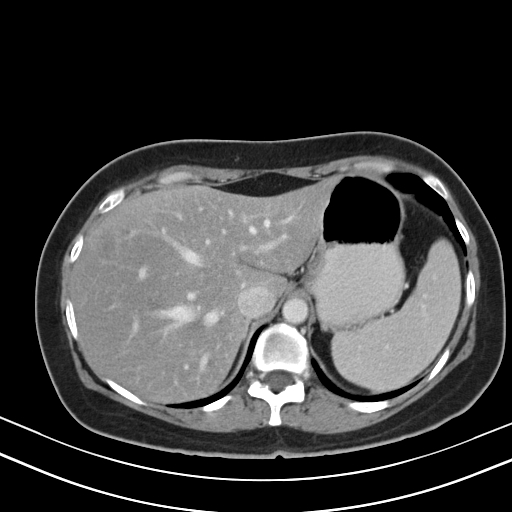
Contrast-enhanced abdominal CT, one axial slice; position 36 of 47 along the scan axis; 130 kVp; intravenous contrast given; soft-tissue window (W 400 / L 40 HU); 512 × 512 image matrix. Female patient. Case-level facts recorded for this patient, not image findings: diagnosis: colorectal cancer liver metastases, imaged before liver resection; multiple liver metastases: no; largest metastasis: 3.5 cm; disease in both lobes: no.
Annotated regions visible in this slice (expert manual segmentation):
- hepatic veins: box from (x=154, y=212) to (x=292, y=365) px
- liver: (x=74, y=184)–(x=329, y=400)
- planned liver remnant (the part of the liver to remain after resection): (x=74, y=184)–(x=329, y=400)
- portal vein (with intrahepatic branches): (x=124, y=214)–(x=288, y=345)
- liver metastasis: (x=101, y=240)–(x=115, y=256)